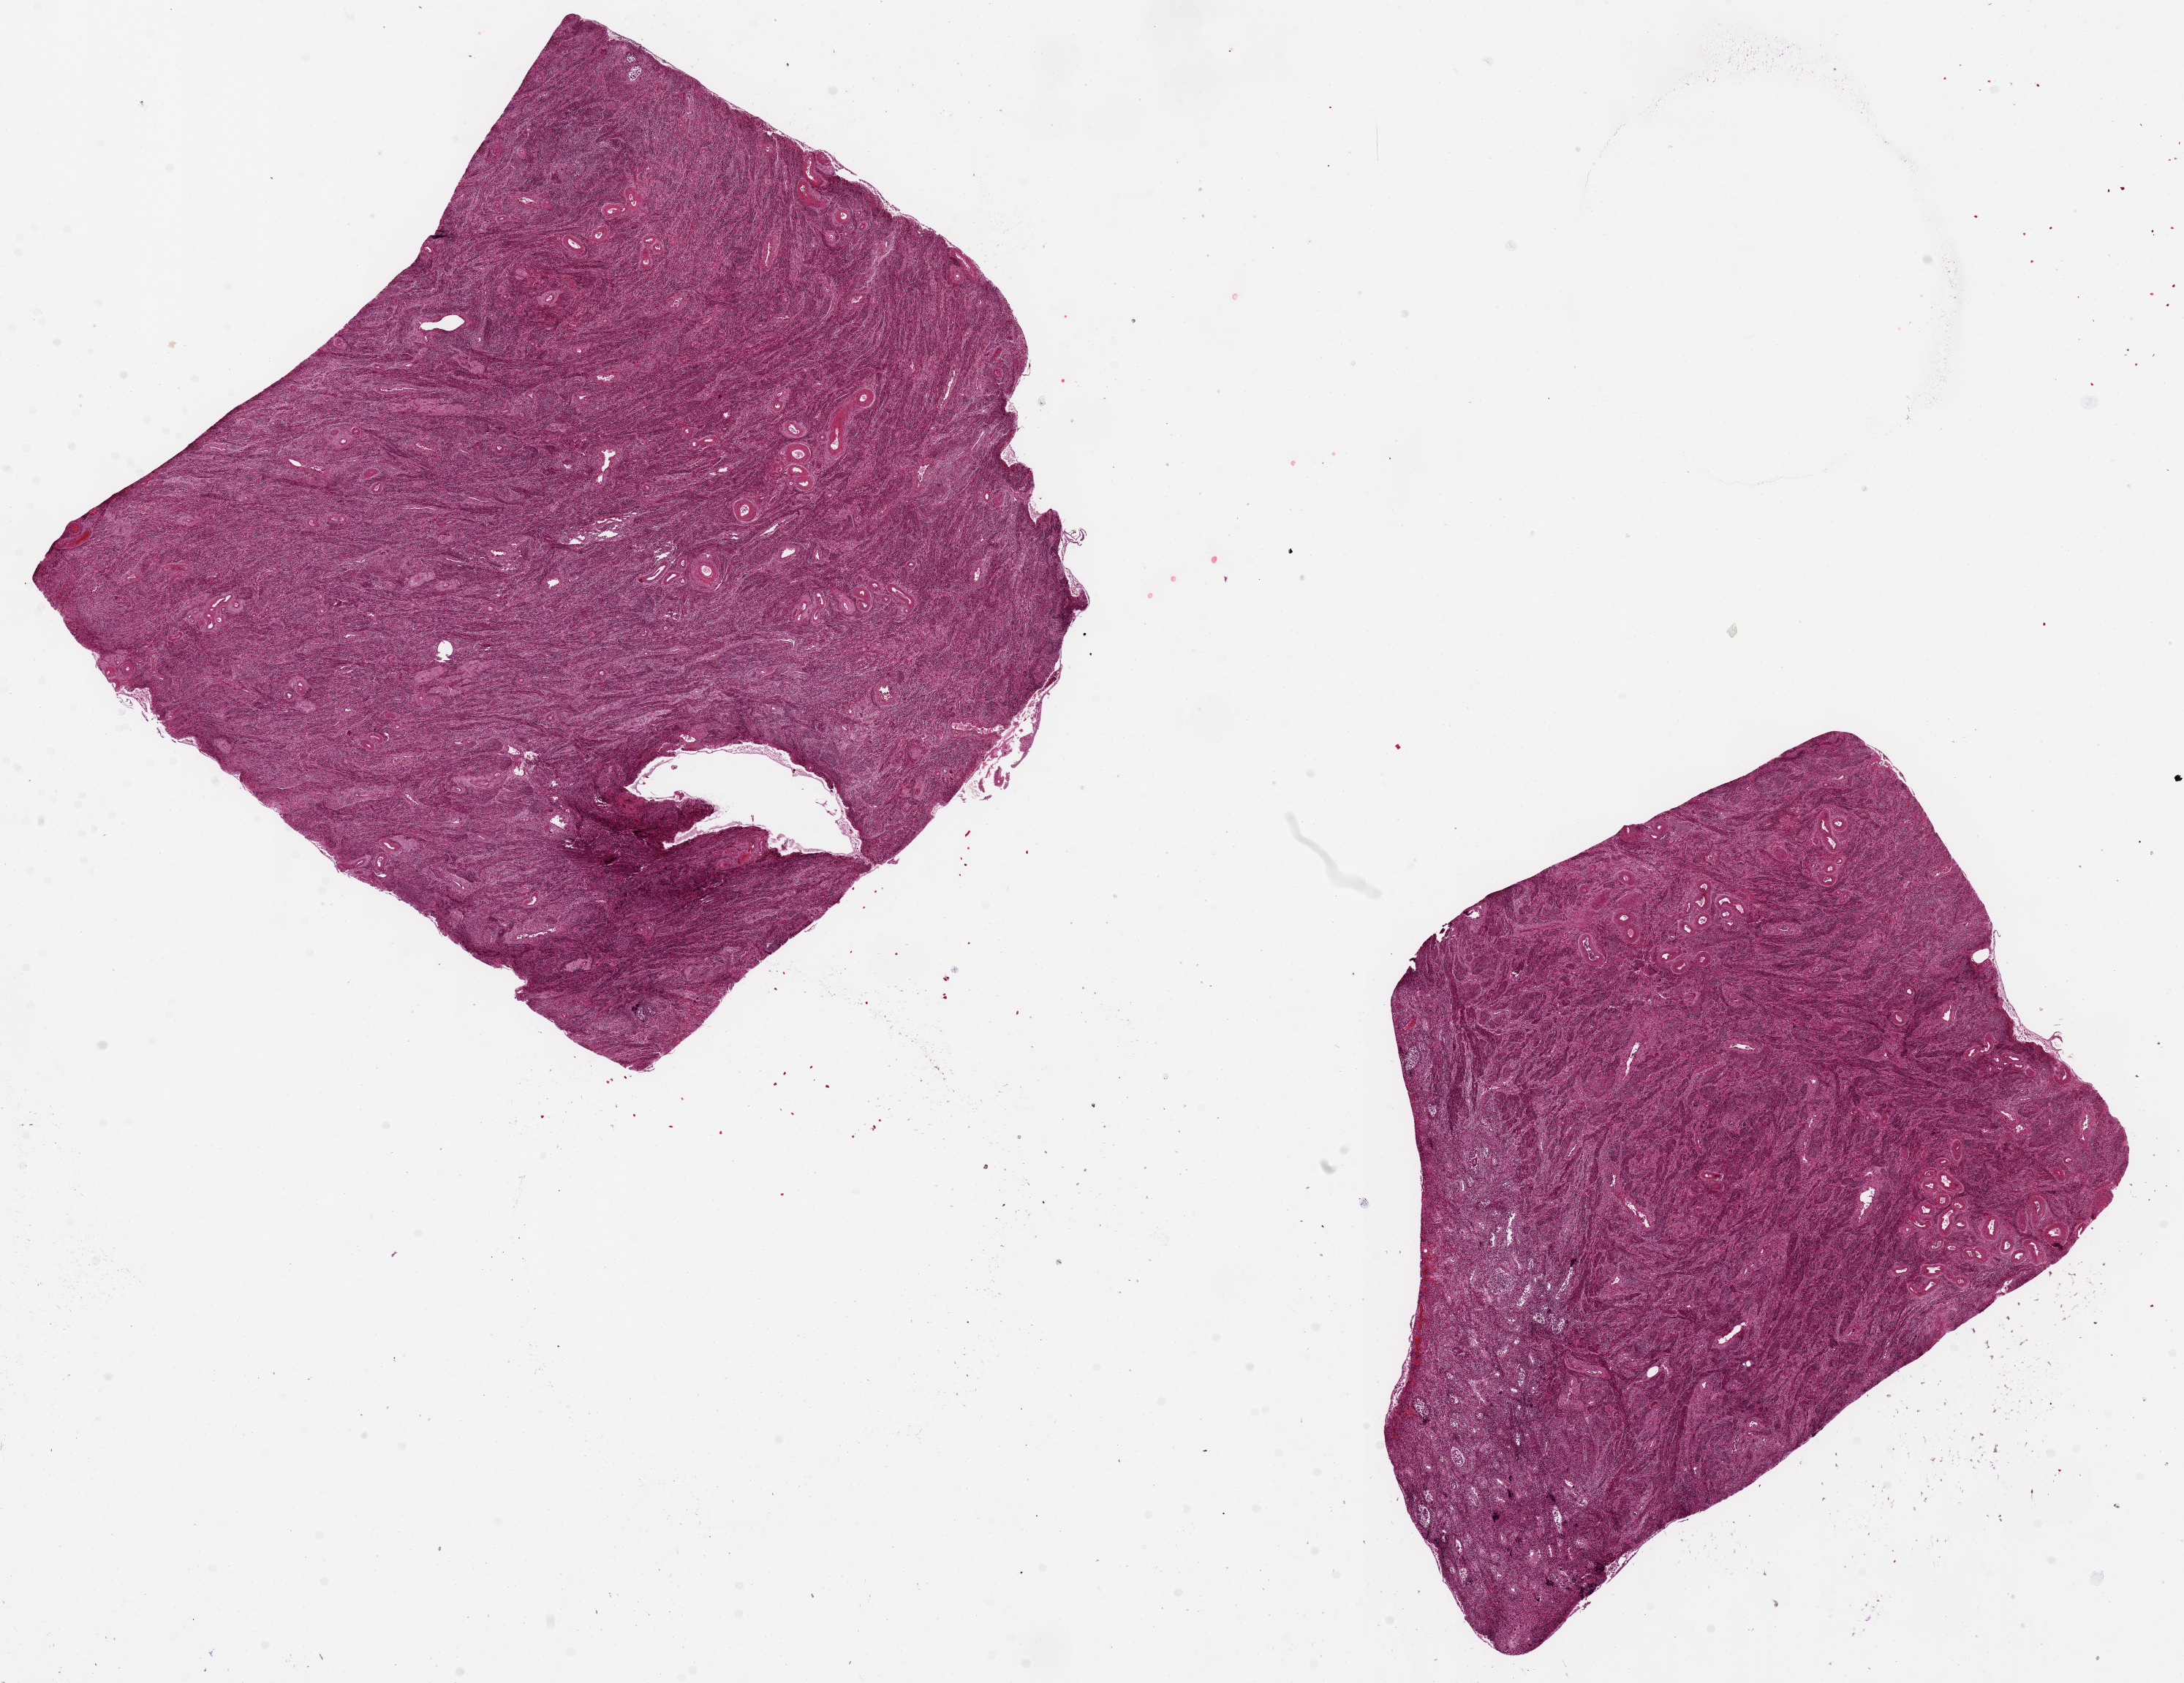
Haematoxylin and eosin whole-slide image, brightfield, a low-resolution overview of the entire scanned area, about 23.6 x 18.2 mm, PAXgene-fixed paraffin-embedded (PFPE) section, section of uterus (target tissue), tissue donor sample. Donor: female.
- review note (as recorded): 2 ~9x8mm aliquots. No viable endometrium; completely autolyzed focus along edge of one aliquot